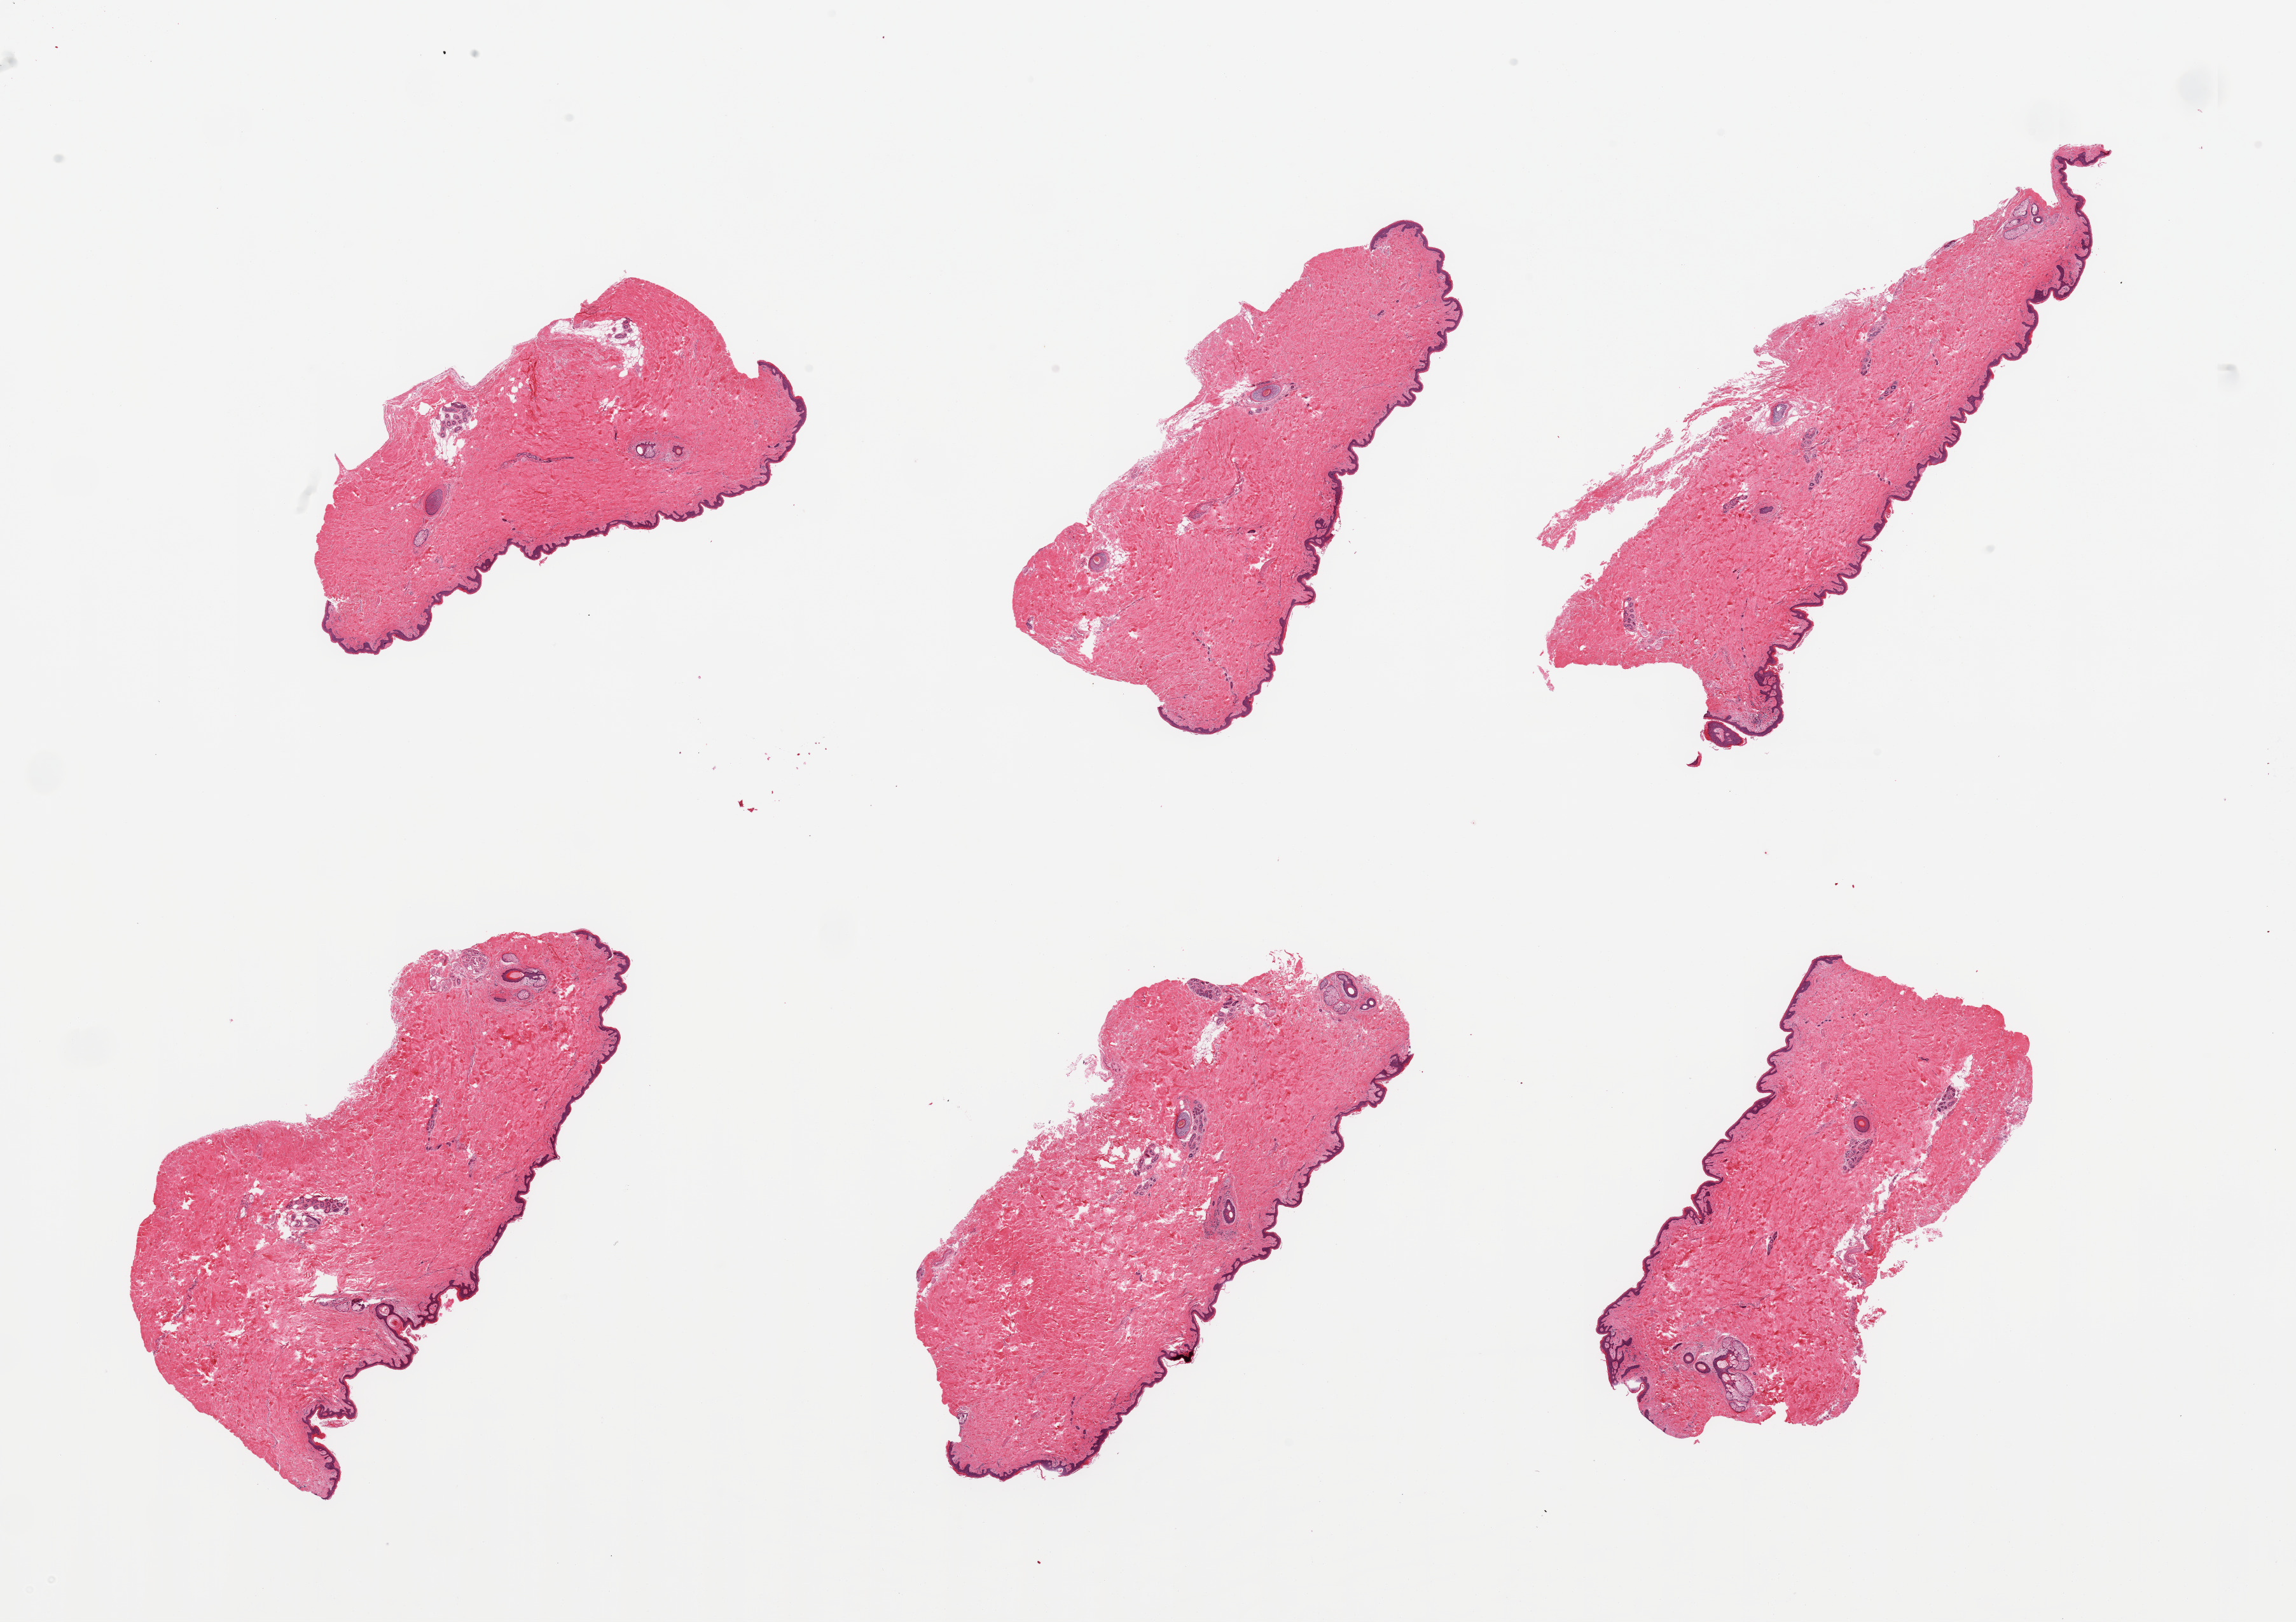
Whole-slide image, haematoxylin and eosin stain — a low-resolution overview of the entire scanned area, about 28.5 x 20.2 mm. PAXgene-fixed paraffin-embedded (PFPE) section. Section of skin of suprapubic region (target tissue). Donor tissue sample.
* pathologist's review note for this sample: 6 pieces, trace dermal fat; squamous epithelium is ~35microns